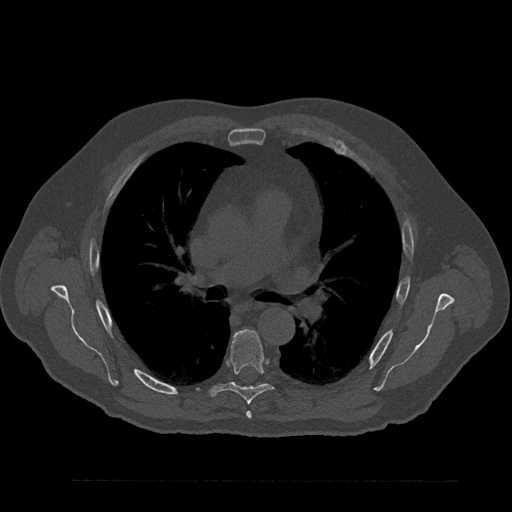
CT including the spine, one axial slice; position 557 of 797 along the scan axis; reconstruction kernel Br40s/3; 120 kVp; bone window (W 1800 / L 400 HU); 512 × 512 image matrix, field of view 430 × 430 mm. Male patient, age 61 years. Case-level facts recorded for this patient, not image findings: primary cancer: prostate.
Outlined on this slice (semi-automatically segmented with operator editing):
- T5 vertebra: bounding box [x1, y1, x2, y2] px = [246, 411, 252, 419]
- T6 vertebra: [208, 329, 274, 405]